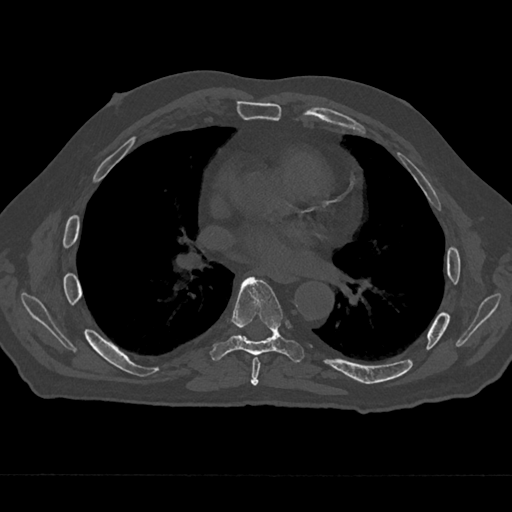
CT including the spine, one axial slice; reconstruction kernel Br40s/3; 120 kVp; bone window (W 1800 / L 400 HU); 0.5 mm slice thickness; 512 × 512 image matrix, field of view 377 × 377 mm. Male patient, age 75 years. Case-level facts recorded for this patient, not image findings: primary cancer: renal; vertebrae with lytic lesions (as recorded): T4.
Annotated regions visible in this slice (semi-automatic segmentation, software-assisted and operator-edited):
- T6 vertebra: bounding box [x1, y1, x2, y2] px = [251, 357, 260, 386]
- T7 vertebra: [210, 277, 305, 362]